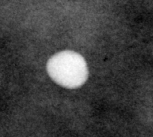
Cropped region of a digitized screen-film mammogram centred on a radiologist-marked abnormality; right breast; CC view.
Calcifications, morphology coarse / round and regular / lucent centered; BI-RADS assessment category 2; subtlety rating 4 on a 1 (subtle) to 5 (obvious) scale; benign; no additional work-up was recommended (benign without callback).